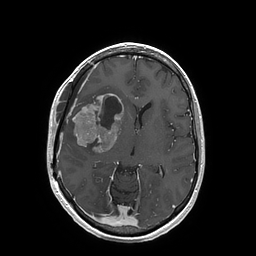
Brain MRI from a brain-tumour surgery series, one axial slice; position 90 of 202 along the scan axis; T1-weighted post-contrast; 256 × 256 image matrix, field of view 250 × 250 mm. From the clinical record (not read from this slice): histopathology: Glioblastoma; WHO grade: 4; IDH mutation: no.
Outlined on this slice (expert manual segmentation):
- tumour: box from (x=73, y=94) to (x=123, y=153) px